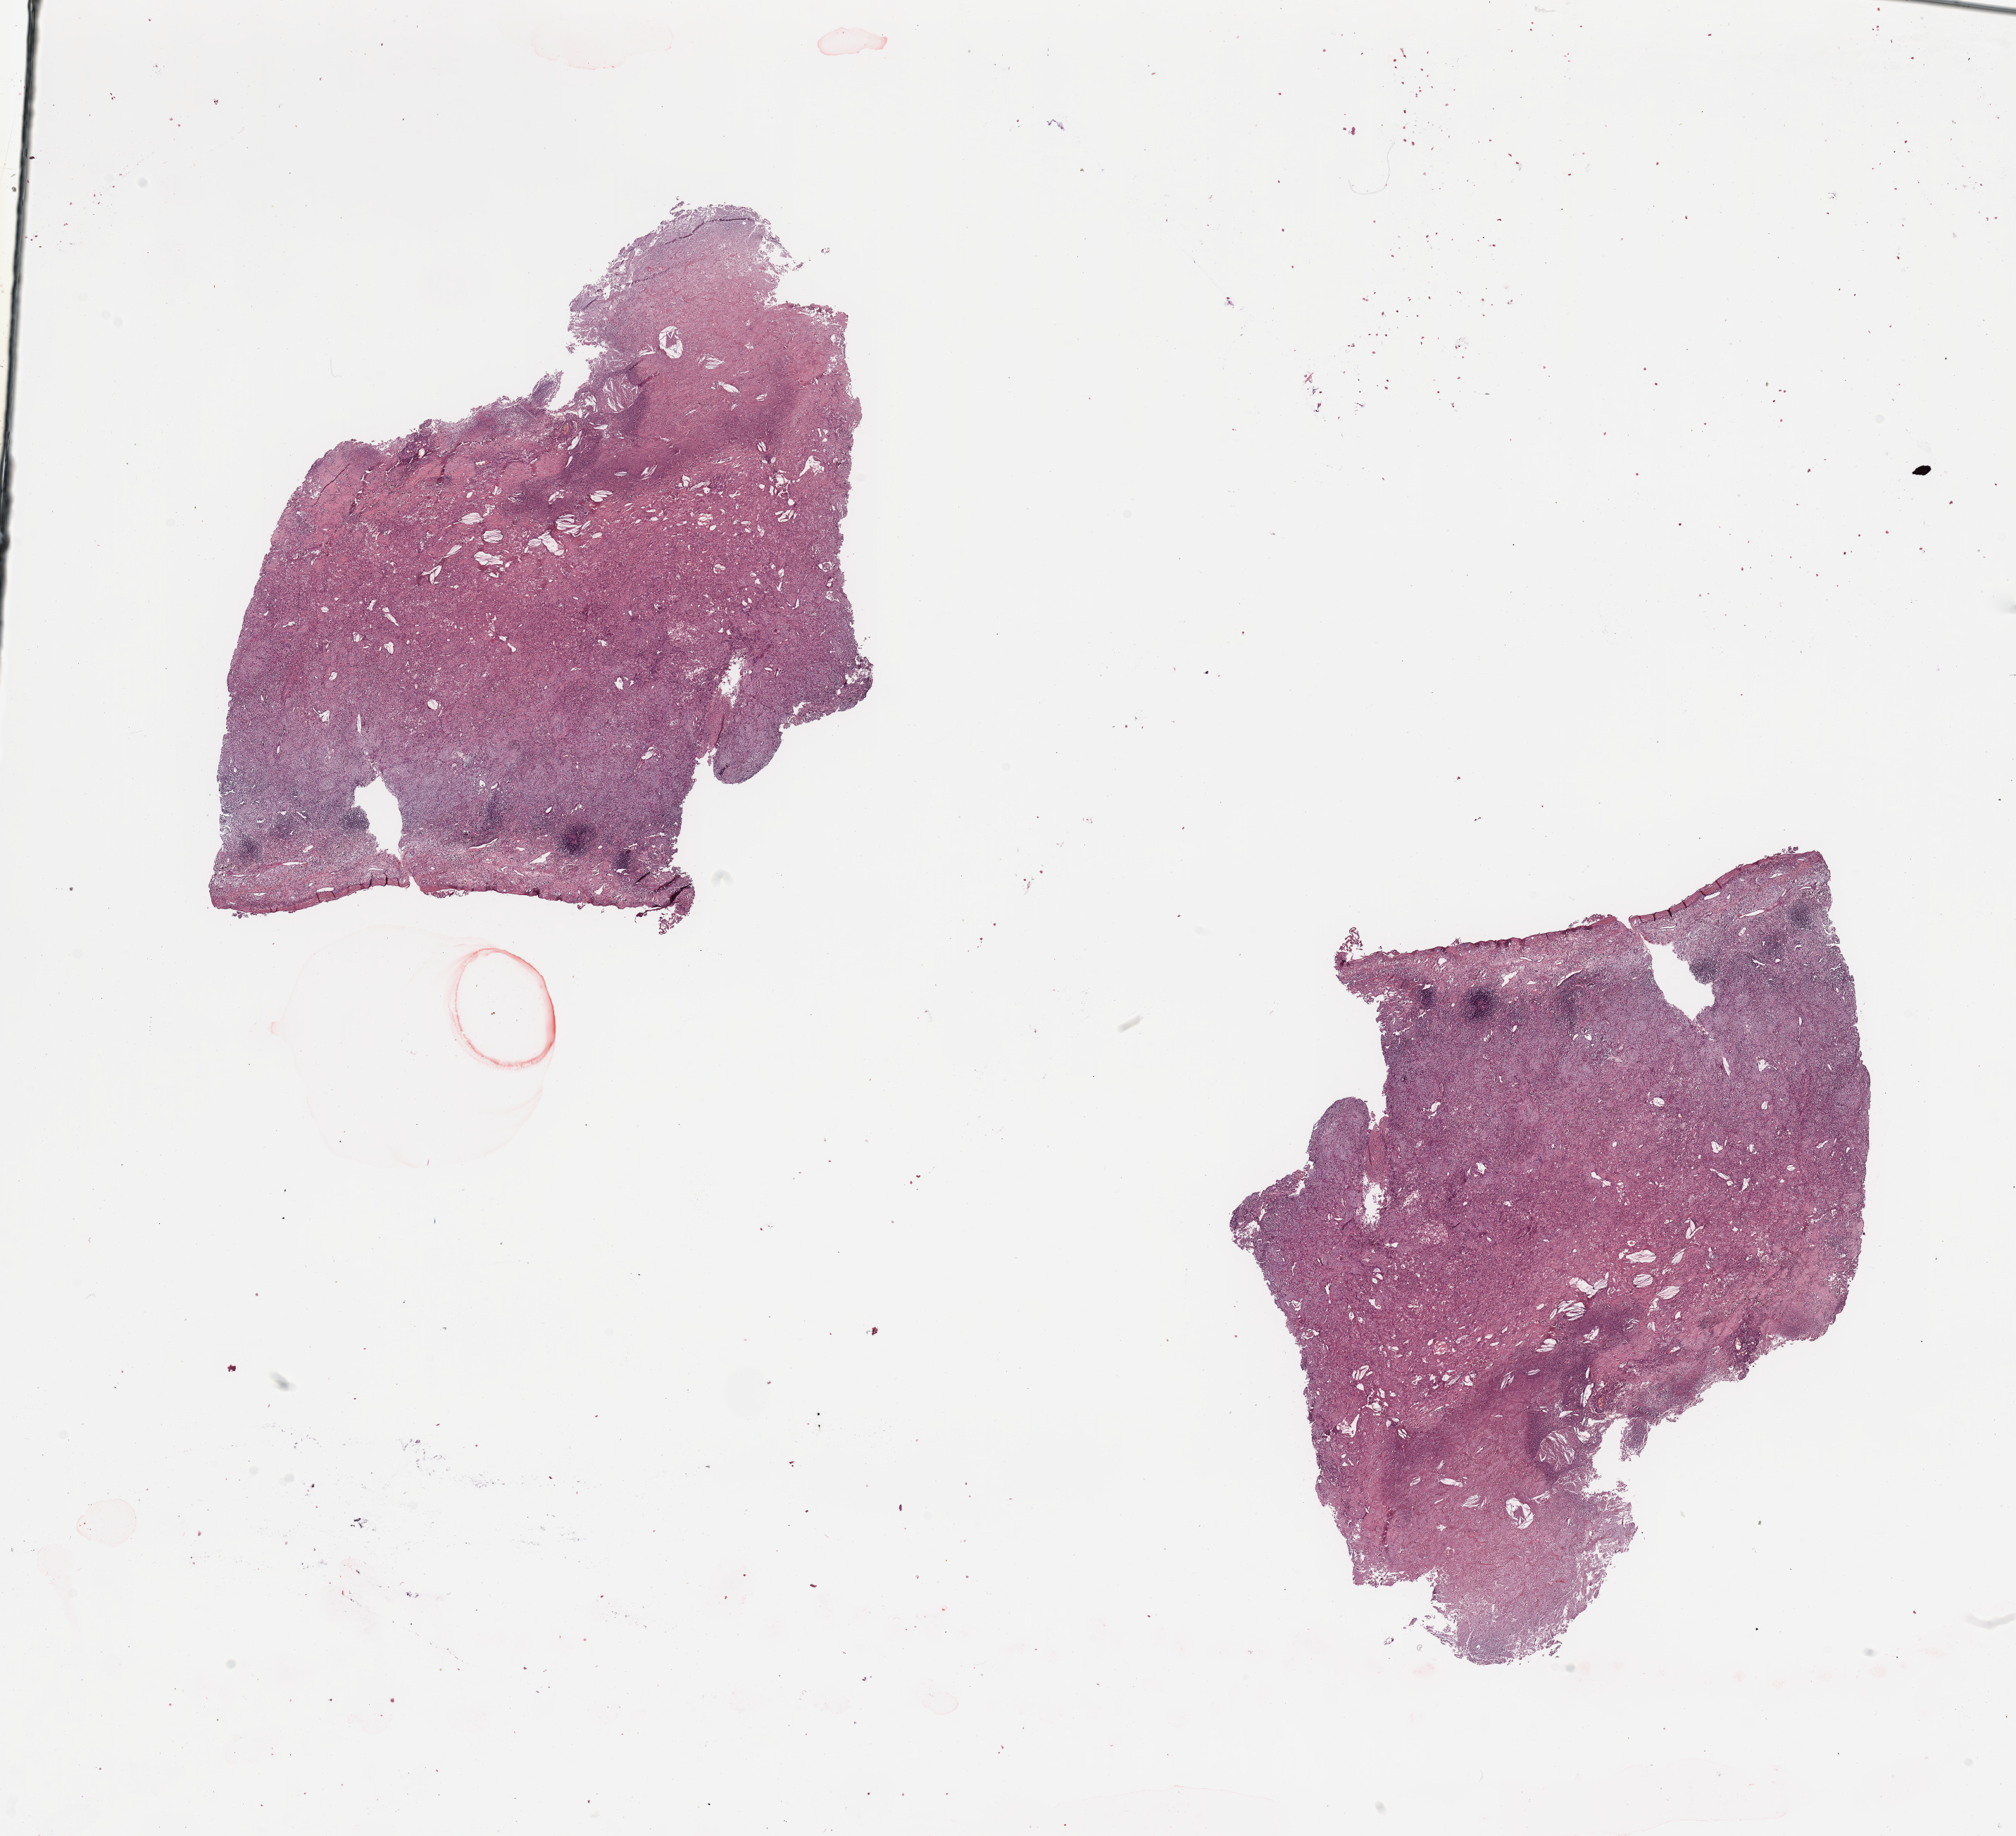
Hematoxylin and eosin (H&E) stained whole-slide image, low-resolution overview of the scanned area, about 22.6 x 20.6 mm (from a 20x scan); tumour tissue sample, sampled site: lung. 78-year-old male patient.
Diagnosis: Squamous cell carcinoma, NOS.